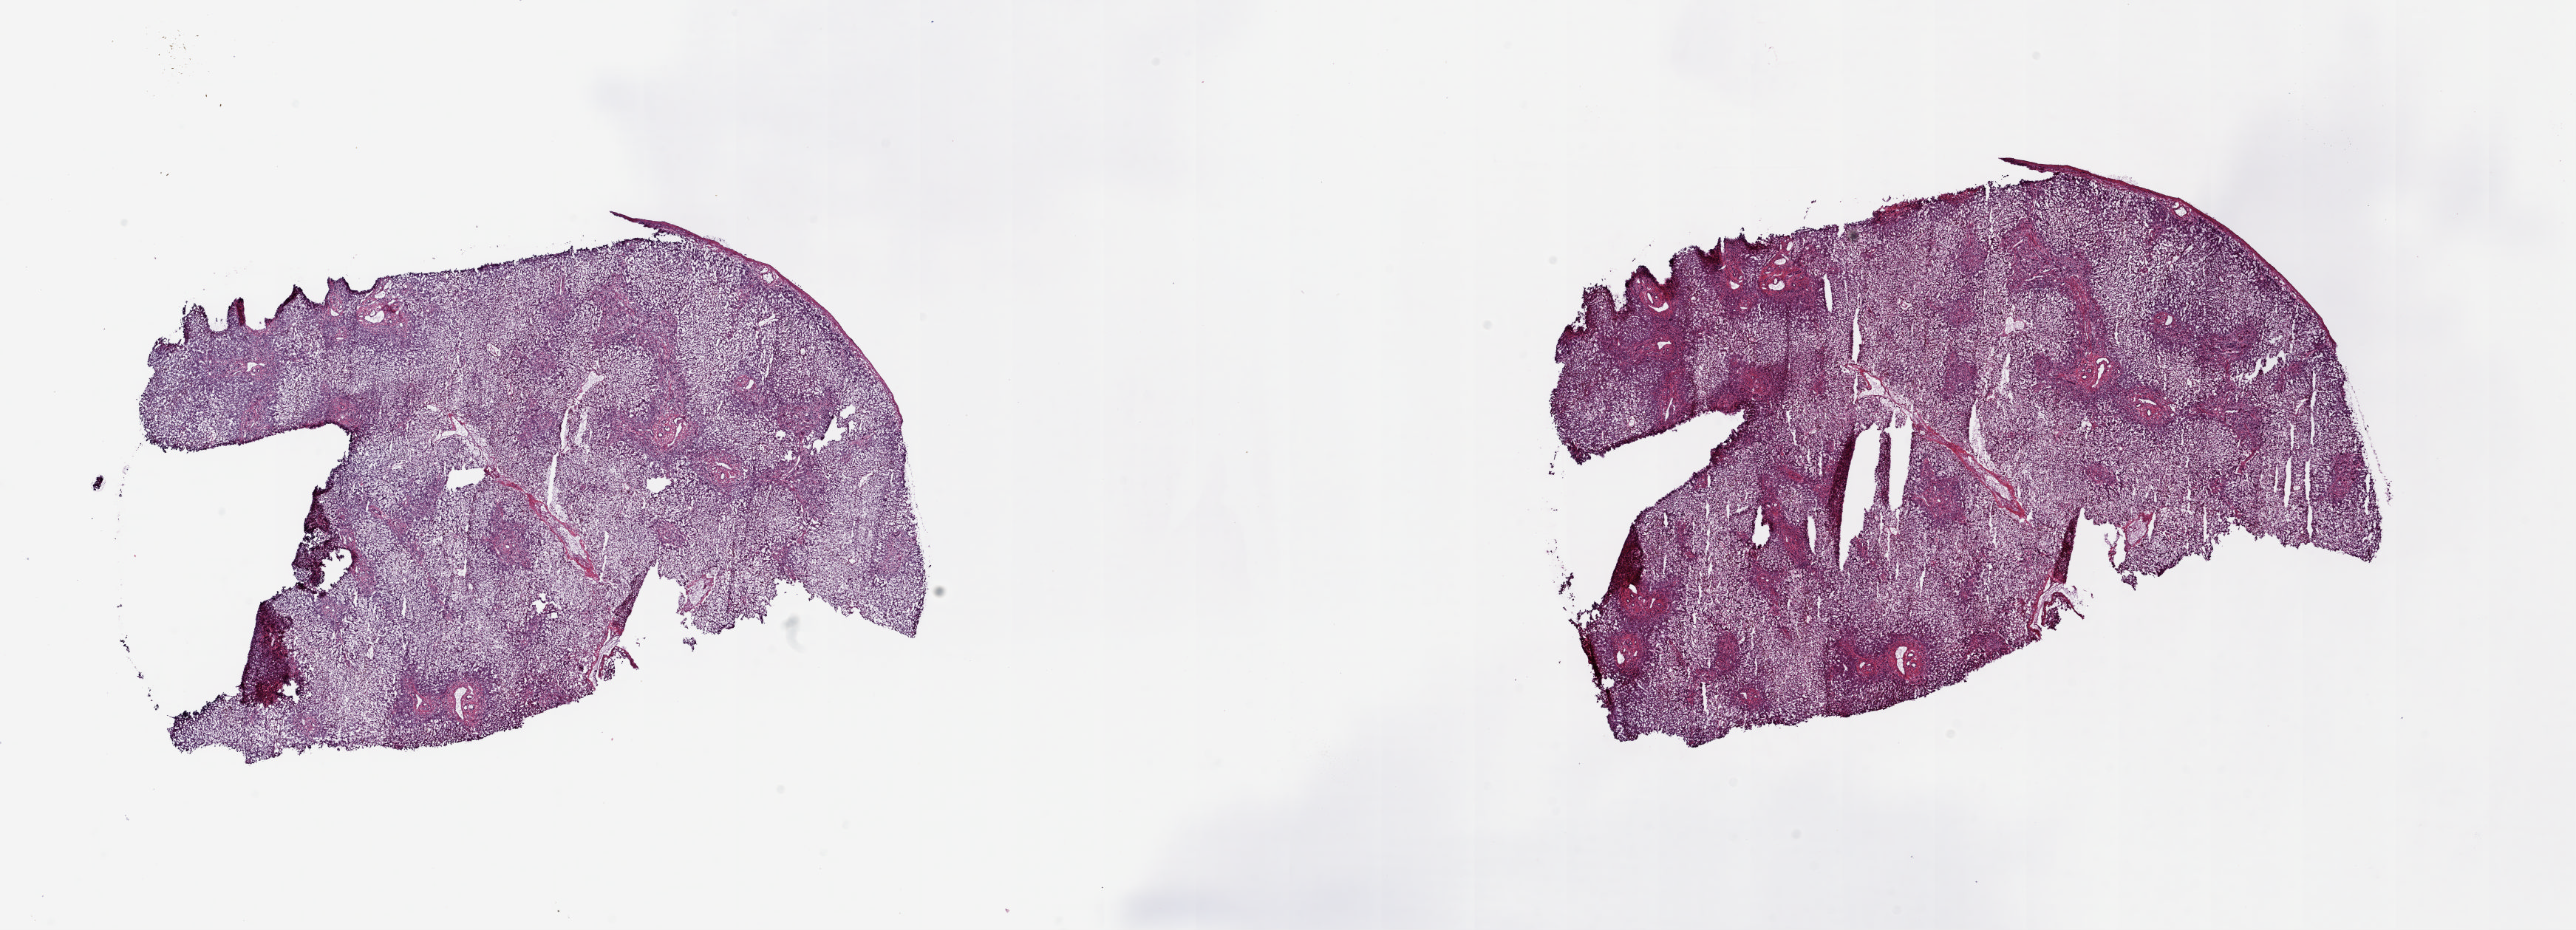
Digitized H&E tissue section (whole slide), low-resolution overview of the scanned area, about 27.7 x 10.0 mm (acquisition: 20x scan), frozen section from the top of the tissue portion, liver, solid tissue normal (non-tumour tissue) sample. Patient: female, age at initial diagnosis 62 years.
This section: solid tissue normal (non-tumour) sample from the same patient. Patient diagnosis: Hepatocellular carcinoma, NOS.